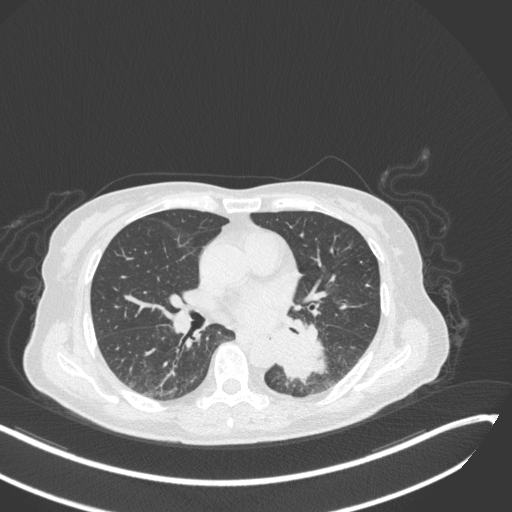
Chest CT, one axial slice; slice 139 of 342 in the series (ordered by position); reconstruction kernel B31f; lung window (W 1500 / L -600 HU); 1 mm slice thickness; 512 × 512 image matrix, field of view 400 × 400 mm. Female patient, age 64 years. Case-level facts recorded for this patient, not image findings: clinical TNM (as recorded): T3 N1 M1; histopathological grade: G3.
Structures marked on this image (rectangle marked by the reading radiologist):
- lung tumour (recorded histology: small cell carcinoma): bounding box [x1, y1, x2, y2] px = [272, 331, 330, 387]